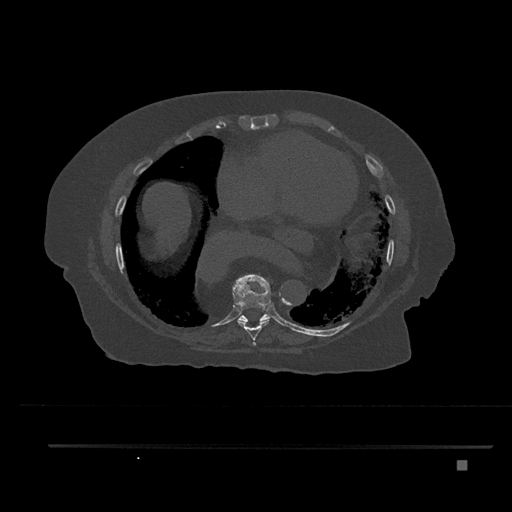
CT including the spine, one axial slice; slice 426 of 797 in the series (ordered by position); 120 kVp; bone window (W 1800 / L 400 HU); 0.5 mm slice thickness; 512 × 512 image matrix, field of view 437 × 437 mm. Female patient, age 76 years. From the clinical record (not read from this slice): primary cancer: lung; vertebrae with lytic lesions (as recorded): T11, L3.
Annotated regions visible in this slice (semi-automatically segmented with operator editing):
- T7 vertebra: bounding box <253,342,256,345> (left, top, right, bottom; pixels)
- T8 vertebra: <233,274,271,346>
- T9 vertebra: <237,311,271,322>